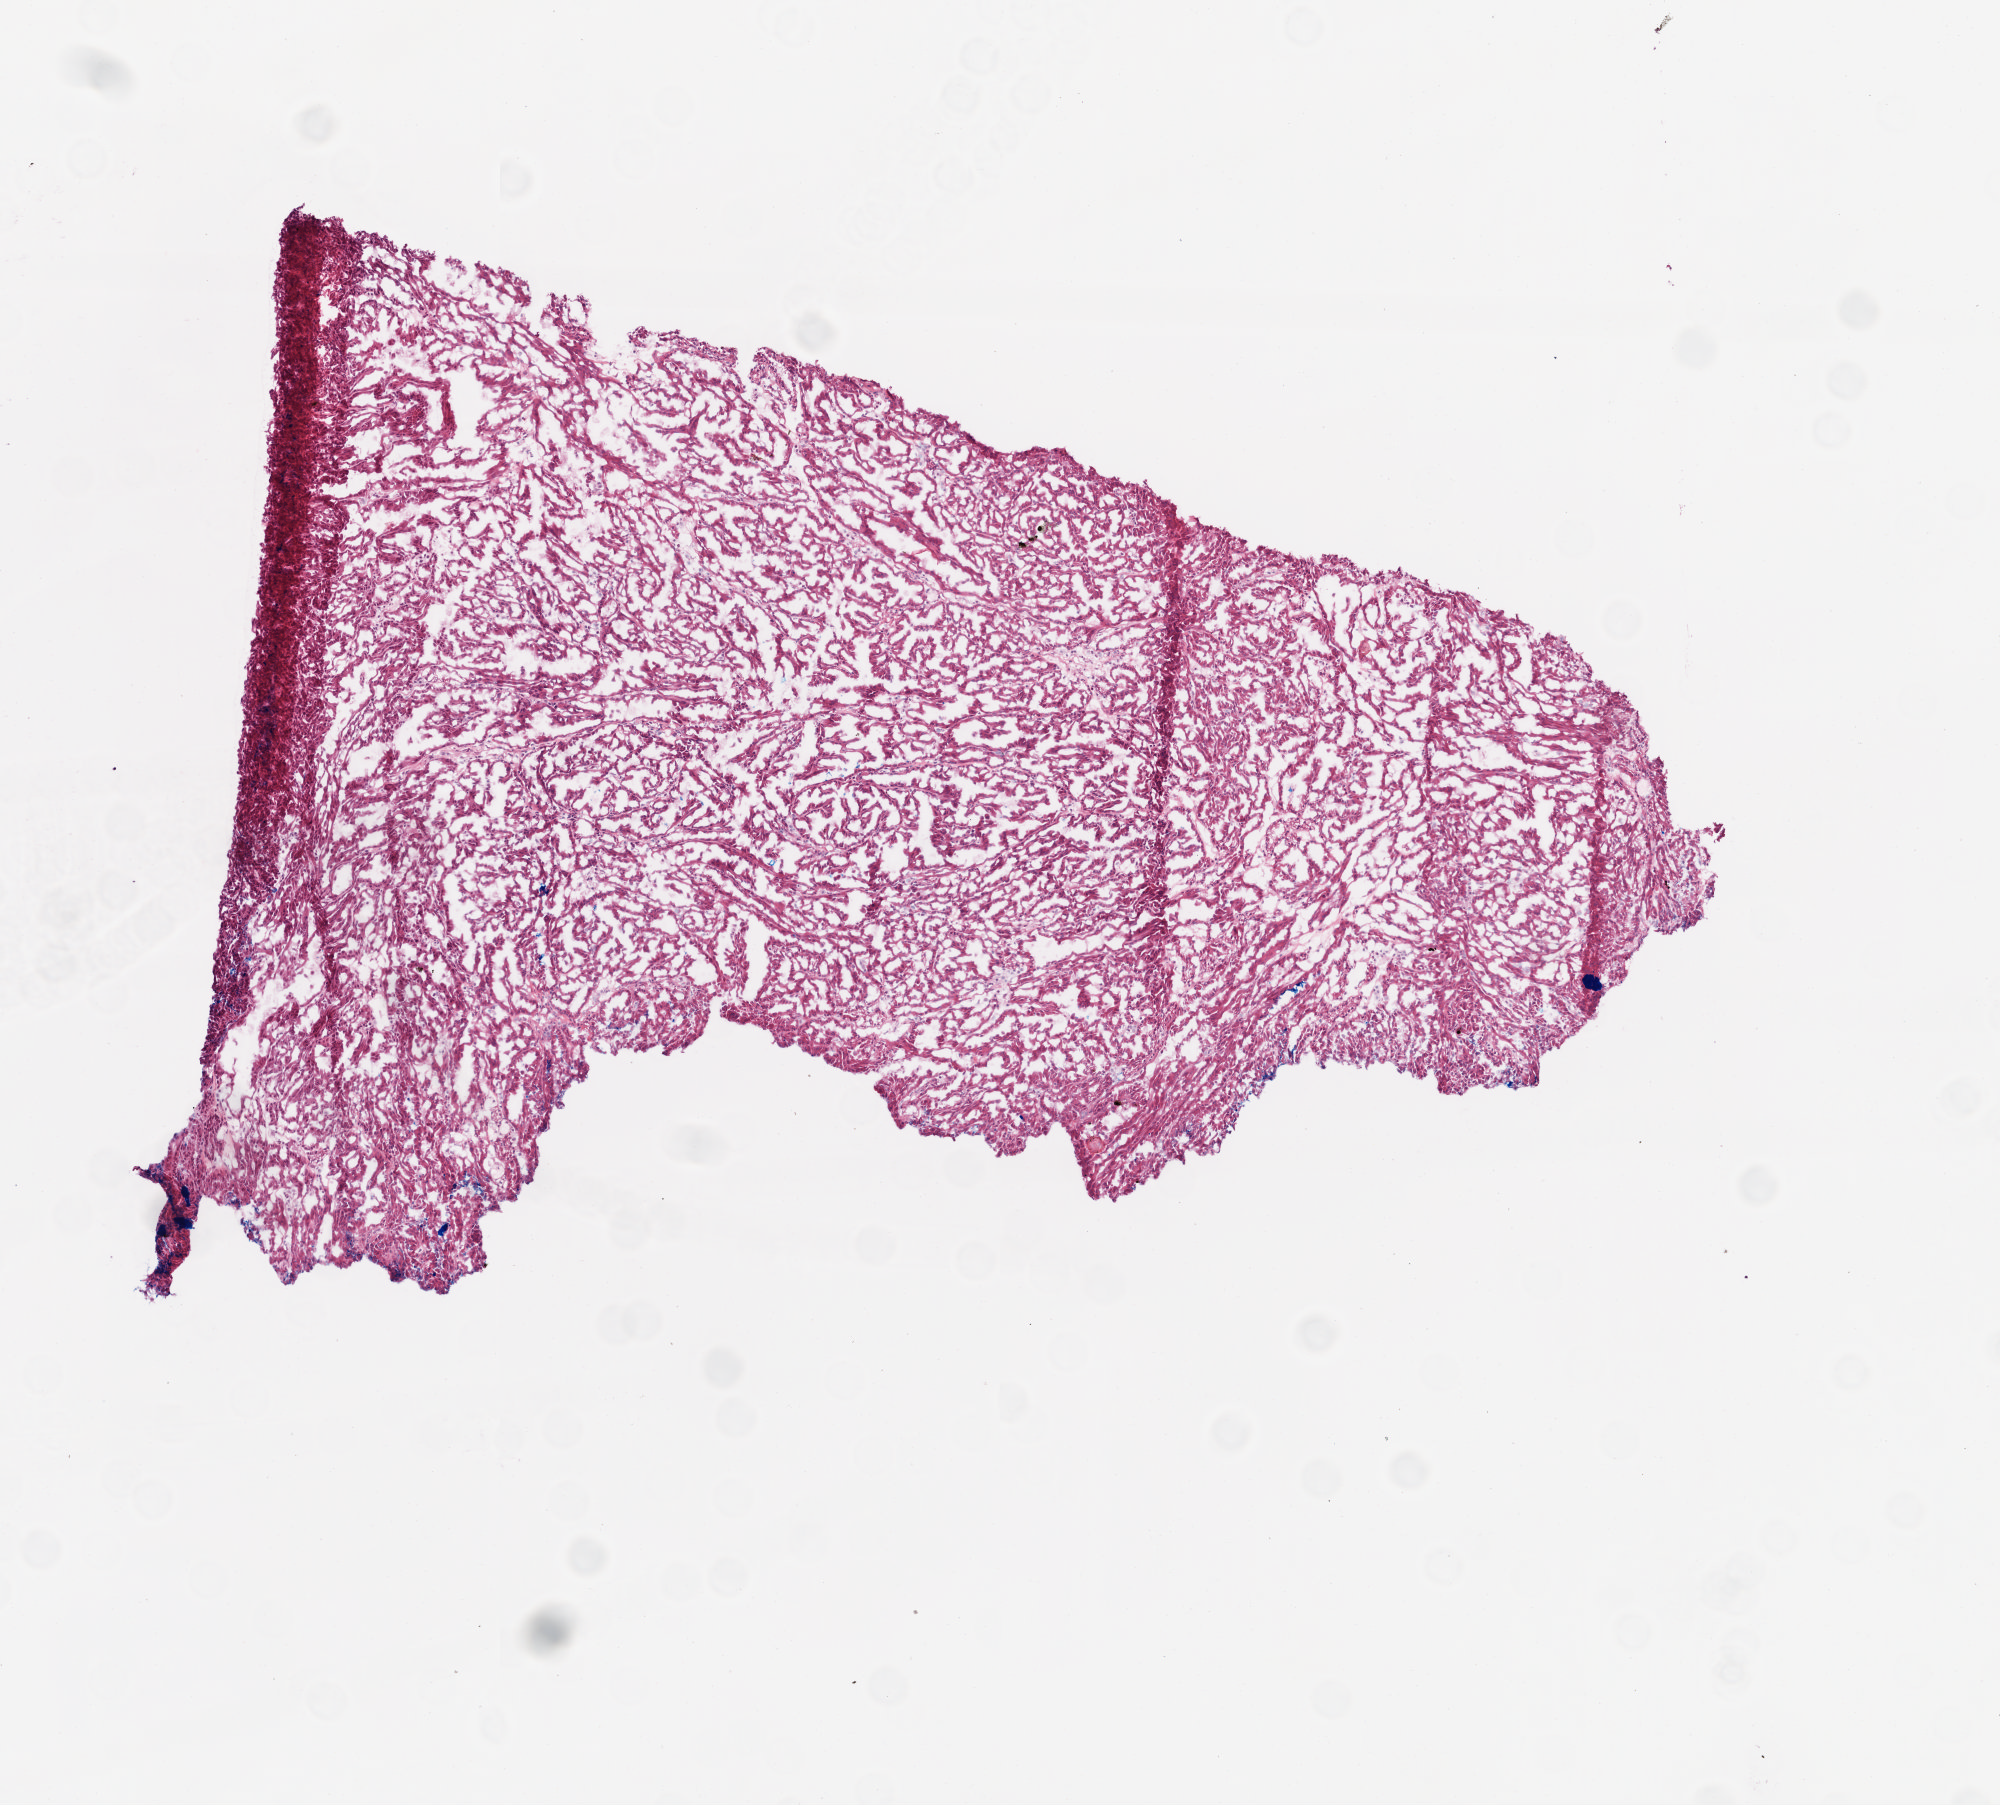
H&E-stained whole-slide image, low-resolution overview of the scanned area, about 4.0 x 3.6 mm (slide scanned at 20x), frozen section from the top of the tissue portion, kidney, primary tumour sample. Male, age 41 years at initial diagnosis. Pathologist review of this section (percent, as recorded): tumour cells 85%, tumour nuclei 75%, normal cells 0%, stromal cells 15%, necrosis 0%.
* histologic diagnosis: Papillary adenocarcinoma, NOS
* laterality: left